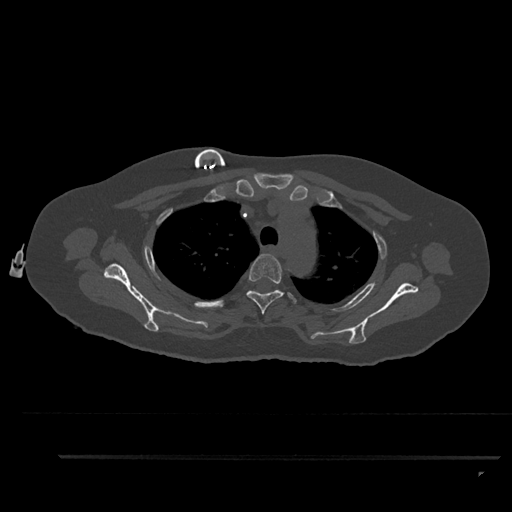
CT including the spine, one axial slice; slice 680 of 797 in the series (ordered by position); reconstruction kernel Br40s/3; bone window (W 1800 / L 400 HU); 0.5 mm slice thickness; 512 × 512 image matrix. Patient: female, 44 years. Case-level facts recorded for this patient, not image findings: primary cancer: renal; vertebrae with lytic lesions (as recorded): L1.
Annotated regions visible in this slice (semi-automatically segmented with operator editing):
- T3 vertebra: box from (x=246, y=254) to (x=297, y=314) px